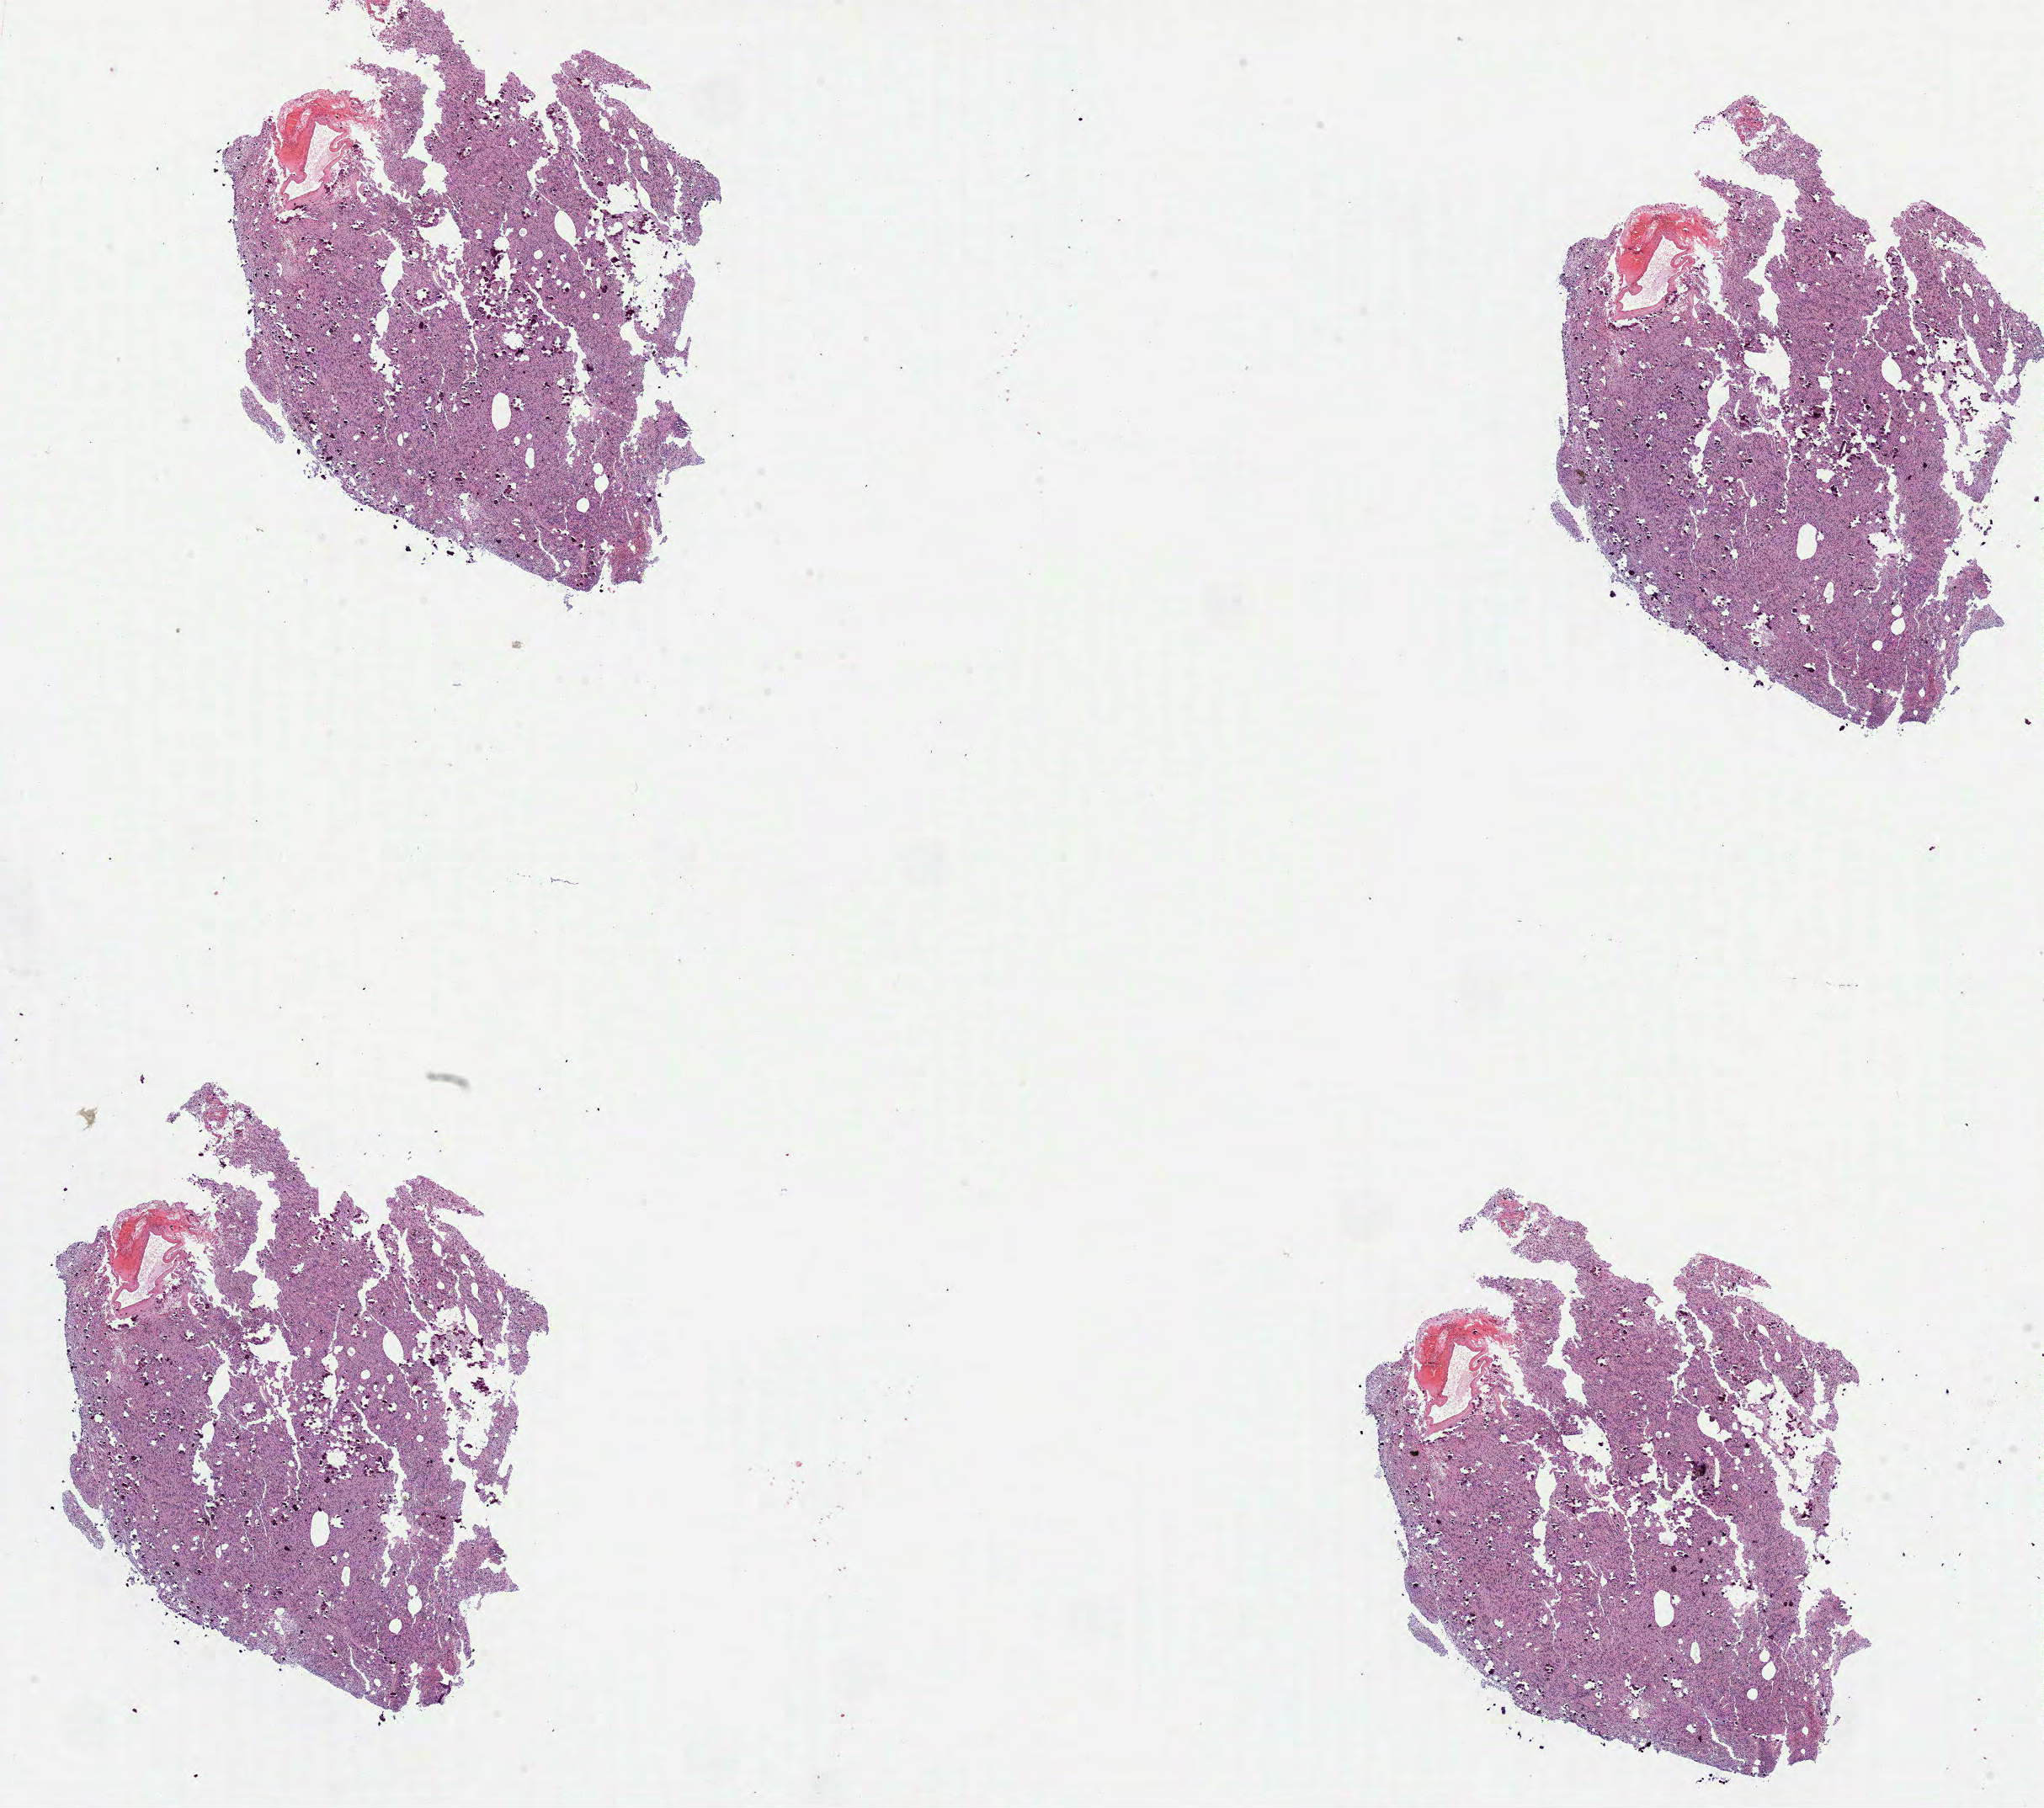
H&E-stained whole-slide image, low-resolution overview of the scanned area, about 19.6 x 17.3 mm (slide scanned at 40x). Formalin-fixed paraffin-embedded (FFPE) diagnostic section. Brain, primary tumour sample. Patient: female, age at initial diagnosis 24 years. Histologic grade: G3 (poorly differentiated).
Pathologic diagnosis: Oligodendroglioma, anaplastic.